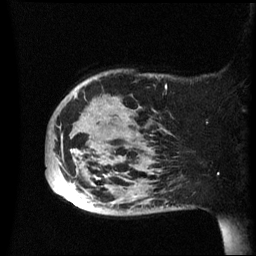
Breast MRI (dynamic contrast-enhanced), one sagittal slice. Position 13 of 60 along the scan axis. Dynamic contrast-enhanced series, image 2 of 3 at this slice position (ordered by acquisition). 1.5 T. TE 4.2 ms, TR 8.4 ms. 2.4 mm slice thickness. 256 × 256 image matrix, field of view 230 × 230 mm. Patient: female, 49 years.
Outlined on this slice (semi-automatically segmented with operator editing):
- analysis volume of interest (the breast-tissue region the enhancement analysis was run in; not a lesion): box from (x=46, y=70) to (x=174, y=215) px
- tumour enhancement mask (voxels above the 70 % enhancement threshold inside the analysis volume of interest): (x=59, y=94)–(x=125, y=196)